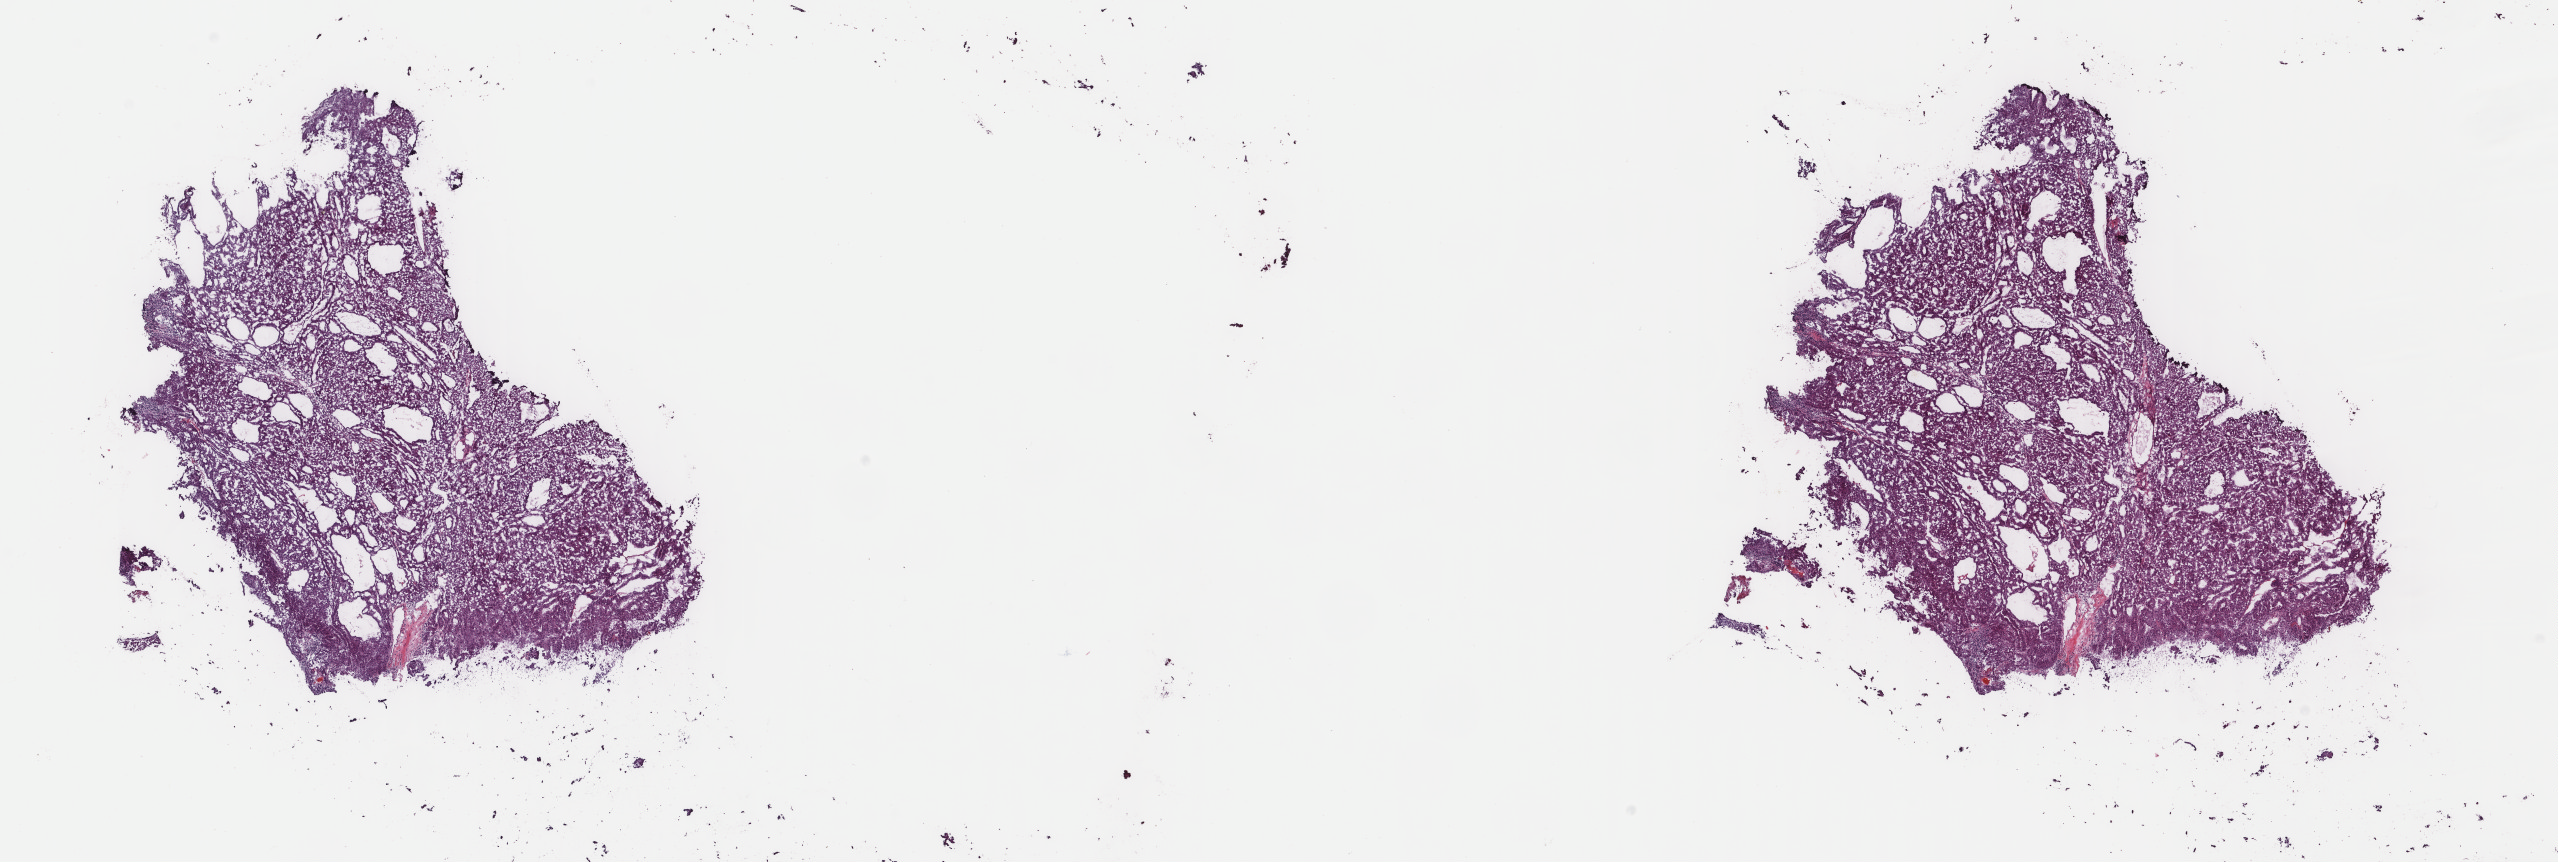
Whole-slide histology image, H&E — a low-resolution overview of the entire scanned area, about 20.3 x 6.8 mm. Frozen section. Sample: primary tumour, liver. Patient: male, age at initial diagnosis 61 years.
Pathologic diagnosis: Hepatocellular carcinoma, NOS.